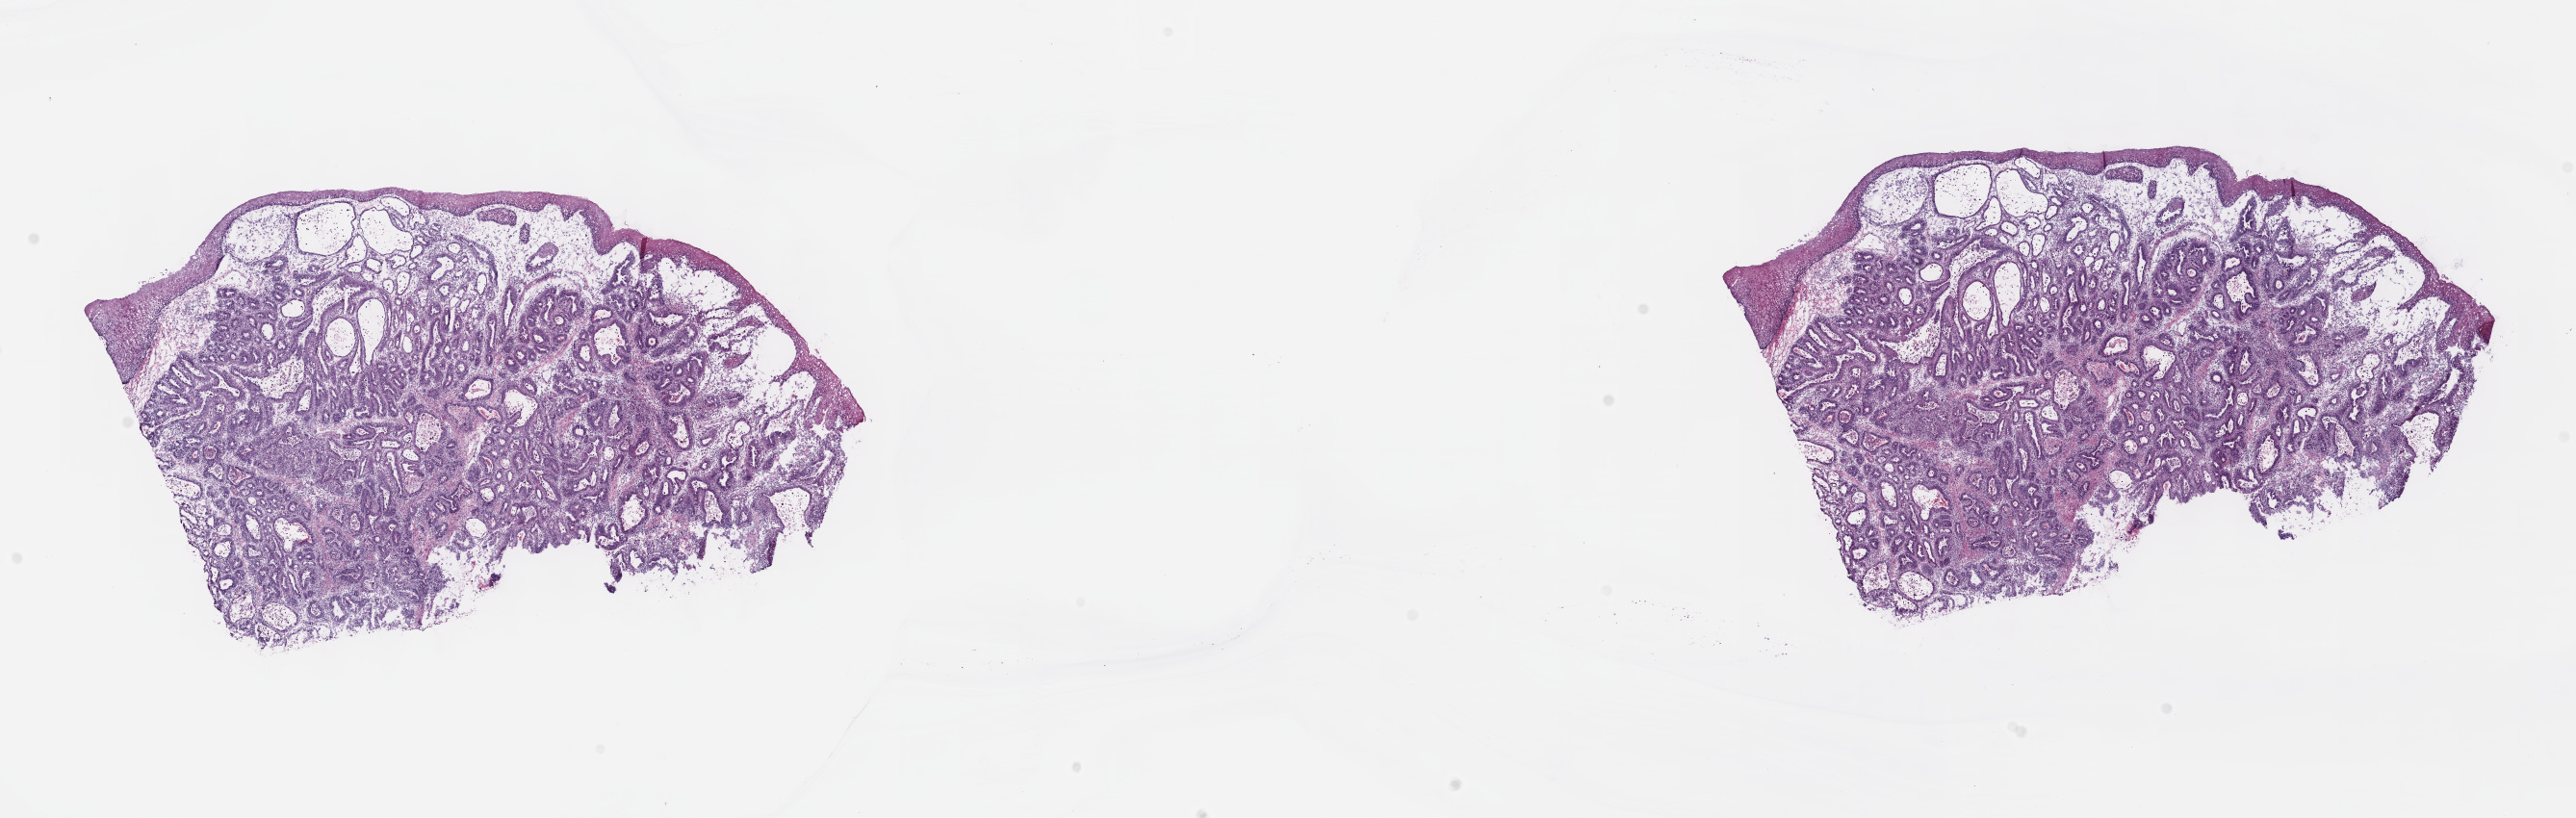
Digitized Hematoxylin and eosin (H&E) stained tissue section (whole slide), low-resolution overview of the scanned area, about 21.6 x 6.9 mm (from a 40x scan). Frozen section from the top of the tissue portion. Esophagus, primary tumour sample. Male patient; age at initial diagnosis 76 years.
Diagnosis: Adenocarcinoma, NOS.